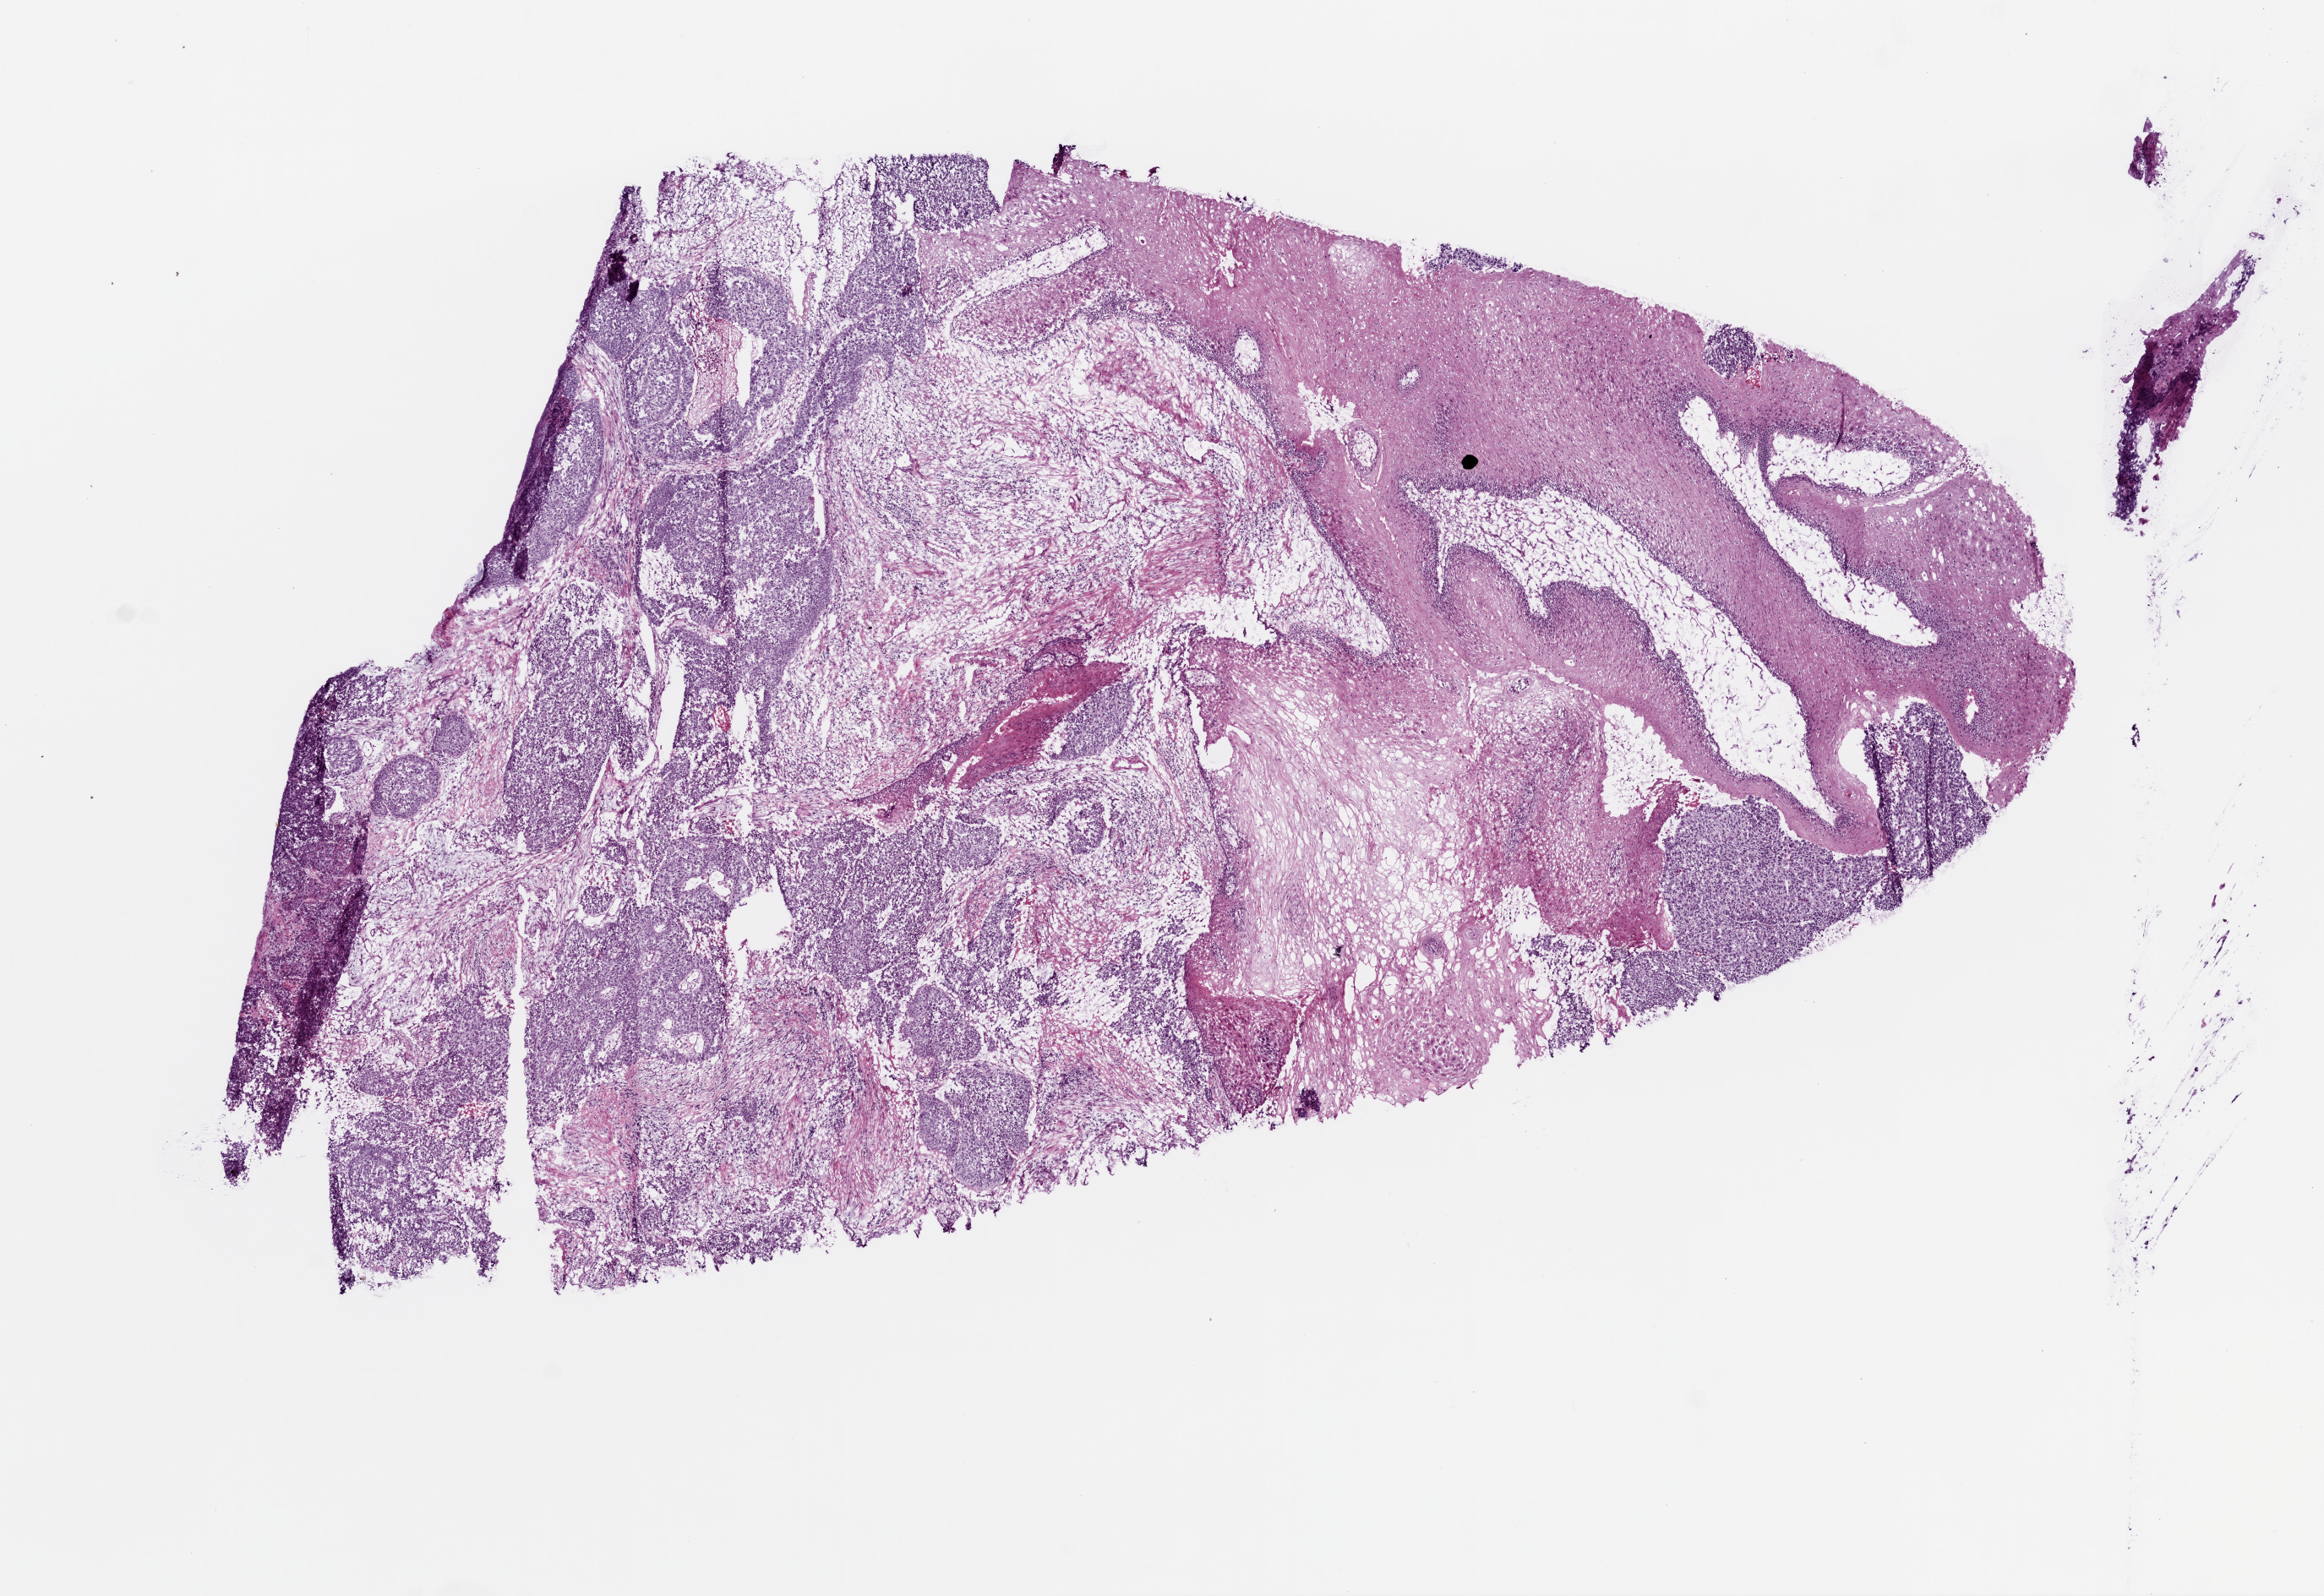
Whole-slide histology image, H&E-stained, whole scanned area (about 11.0 x 7.6 mm, from a 20x scan) shown as a low-resolution overview, frozen section, primary tumour sample from the stomach. Patient: male, age at initial diagnosis 72 years. Histologic grade: G3 (poorly differentiated). Slide review estimates, as recorded: tumour cells 37%, tumour nuclei 75%, normal cells 35%, stromal cells 25%, necrosis 3%.
TNM: T2 N0 M0. AJCC pathologic stage: IB (5th edition). Lymph nodes positive (case pathology): 0 of 23 examined. Pathologic diagnosis: Adenocarcinoma, NOS (cardia, NOS).